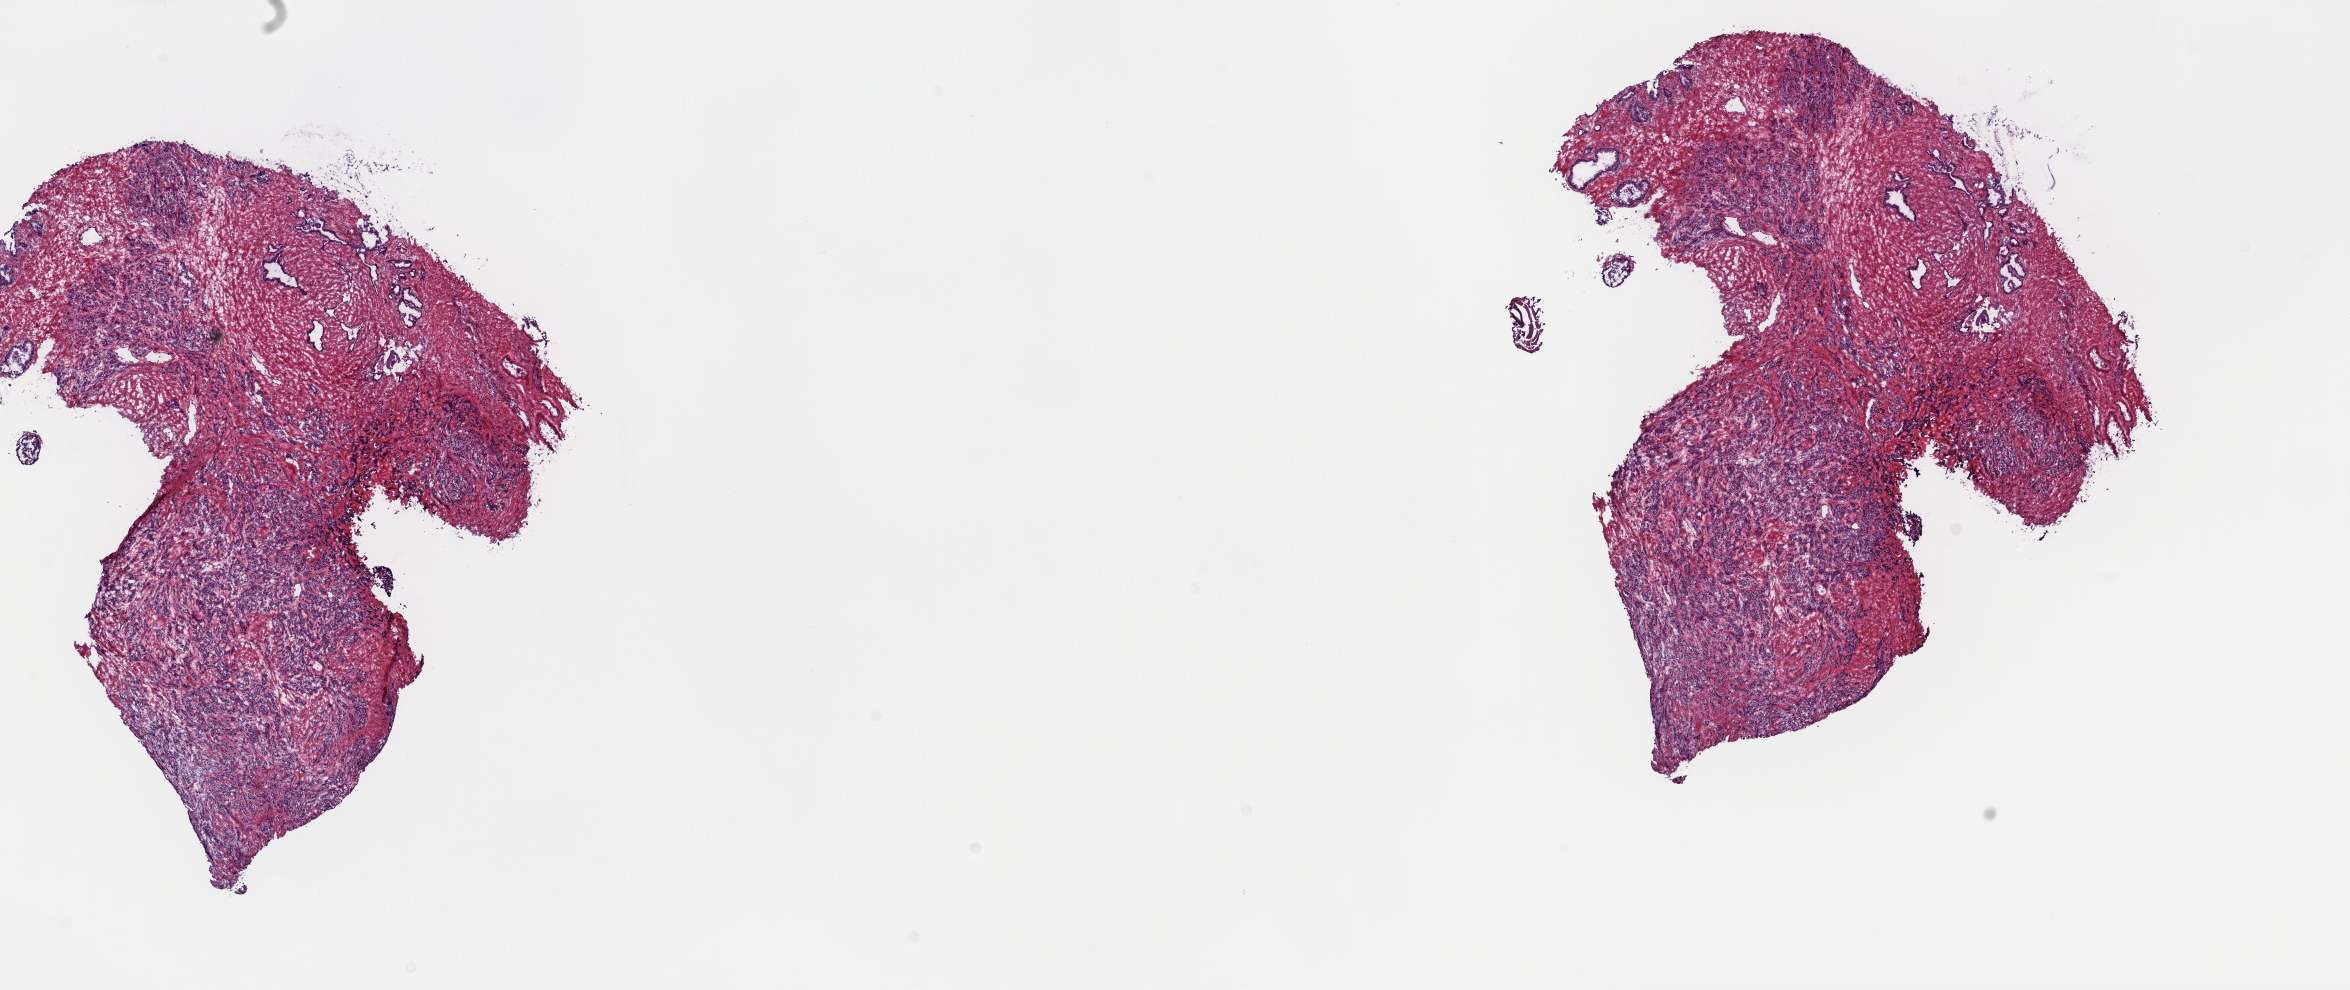
H&E whole-slide image — shown as a low-resolution overview of the whole scanned area (about 18.6 x 7.8 mm, acquisition: 40x scan); frozen section from the top of the tissue portion; primary tumour sample from the prostate. Male, age 57 years at initial diagnosis. Gleason score: 9 (4+5). Slide review estimates, as recorded: tumour cells 80%, tumour nuclei 75%, normal cells 20%, stromal cells 0%, necrosis 0%. Inflammatory infiltration, as recorded: lymphocyte infiltration 0%, monocyte infiltration 0%, neutrophil infiltration 0%.
Pathologic diagnosis: Acinar cell carcinoma (prostate gland). Laterality: bilateral.